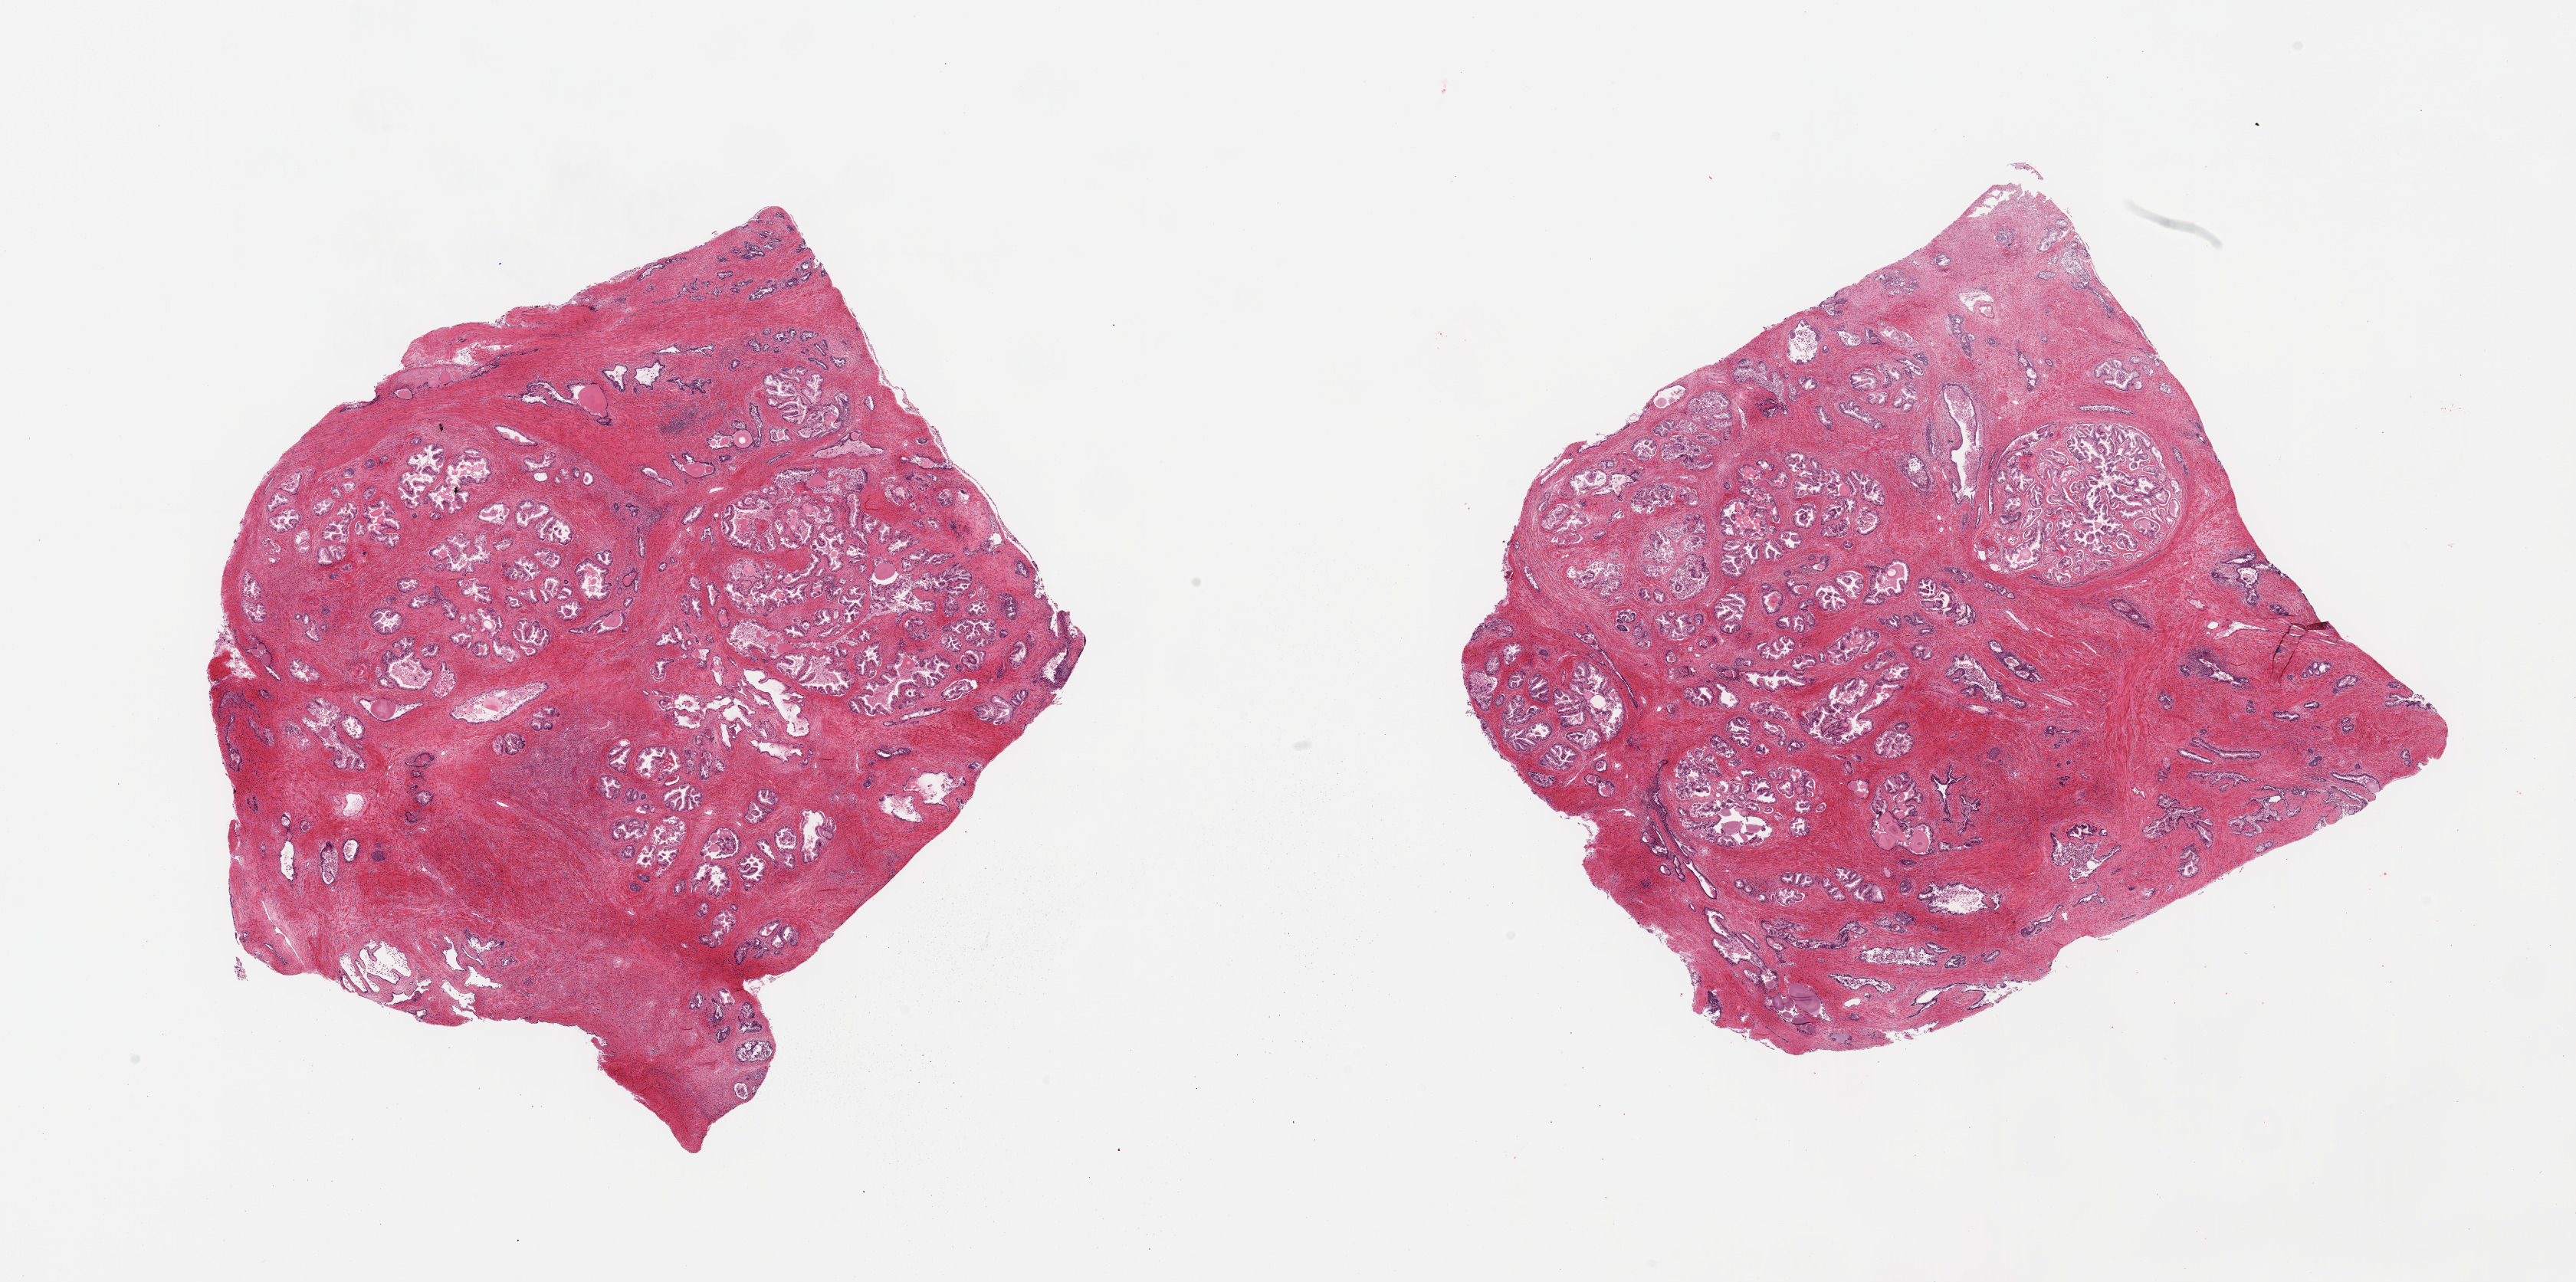
Haematoxylin and eosin whole-slide image — low-resolution overview of the scanned area, about 26.6 x 13.2 mm. PAXgene-fixed paraffin-embedded (PFPE) section. Target tissue: prostate. Donor tissue sample. Male donor.
Reviewer comment on this tissue sample: 2 pieces, some glands approach score 2, hyperplastic pattern.